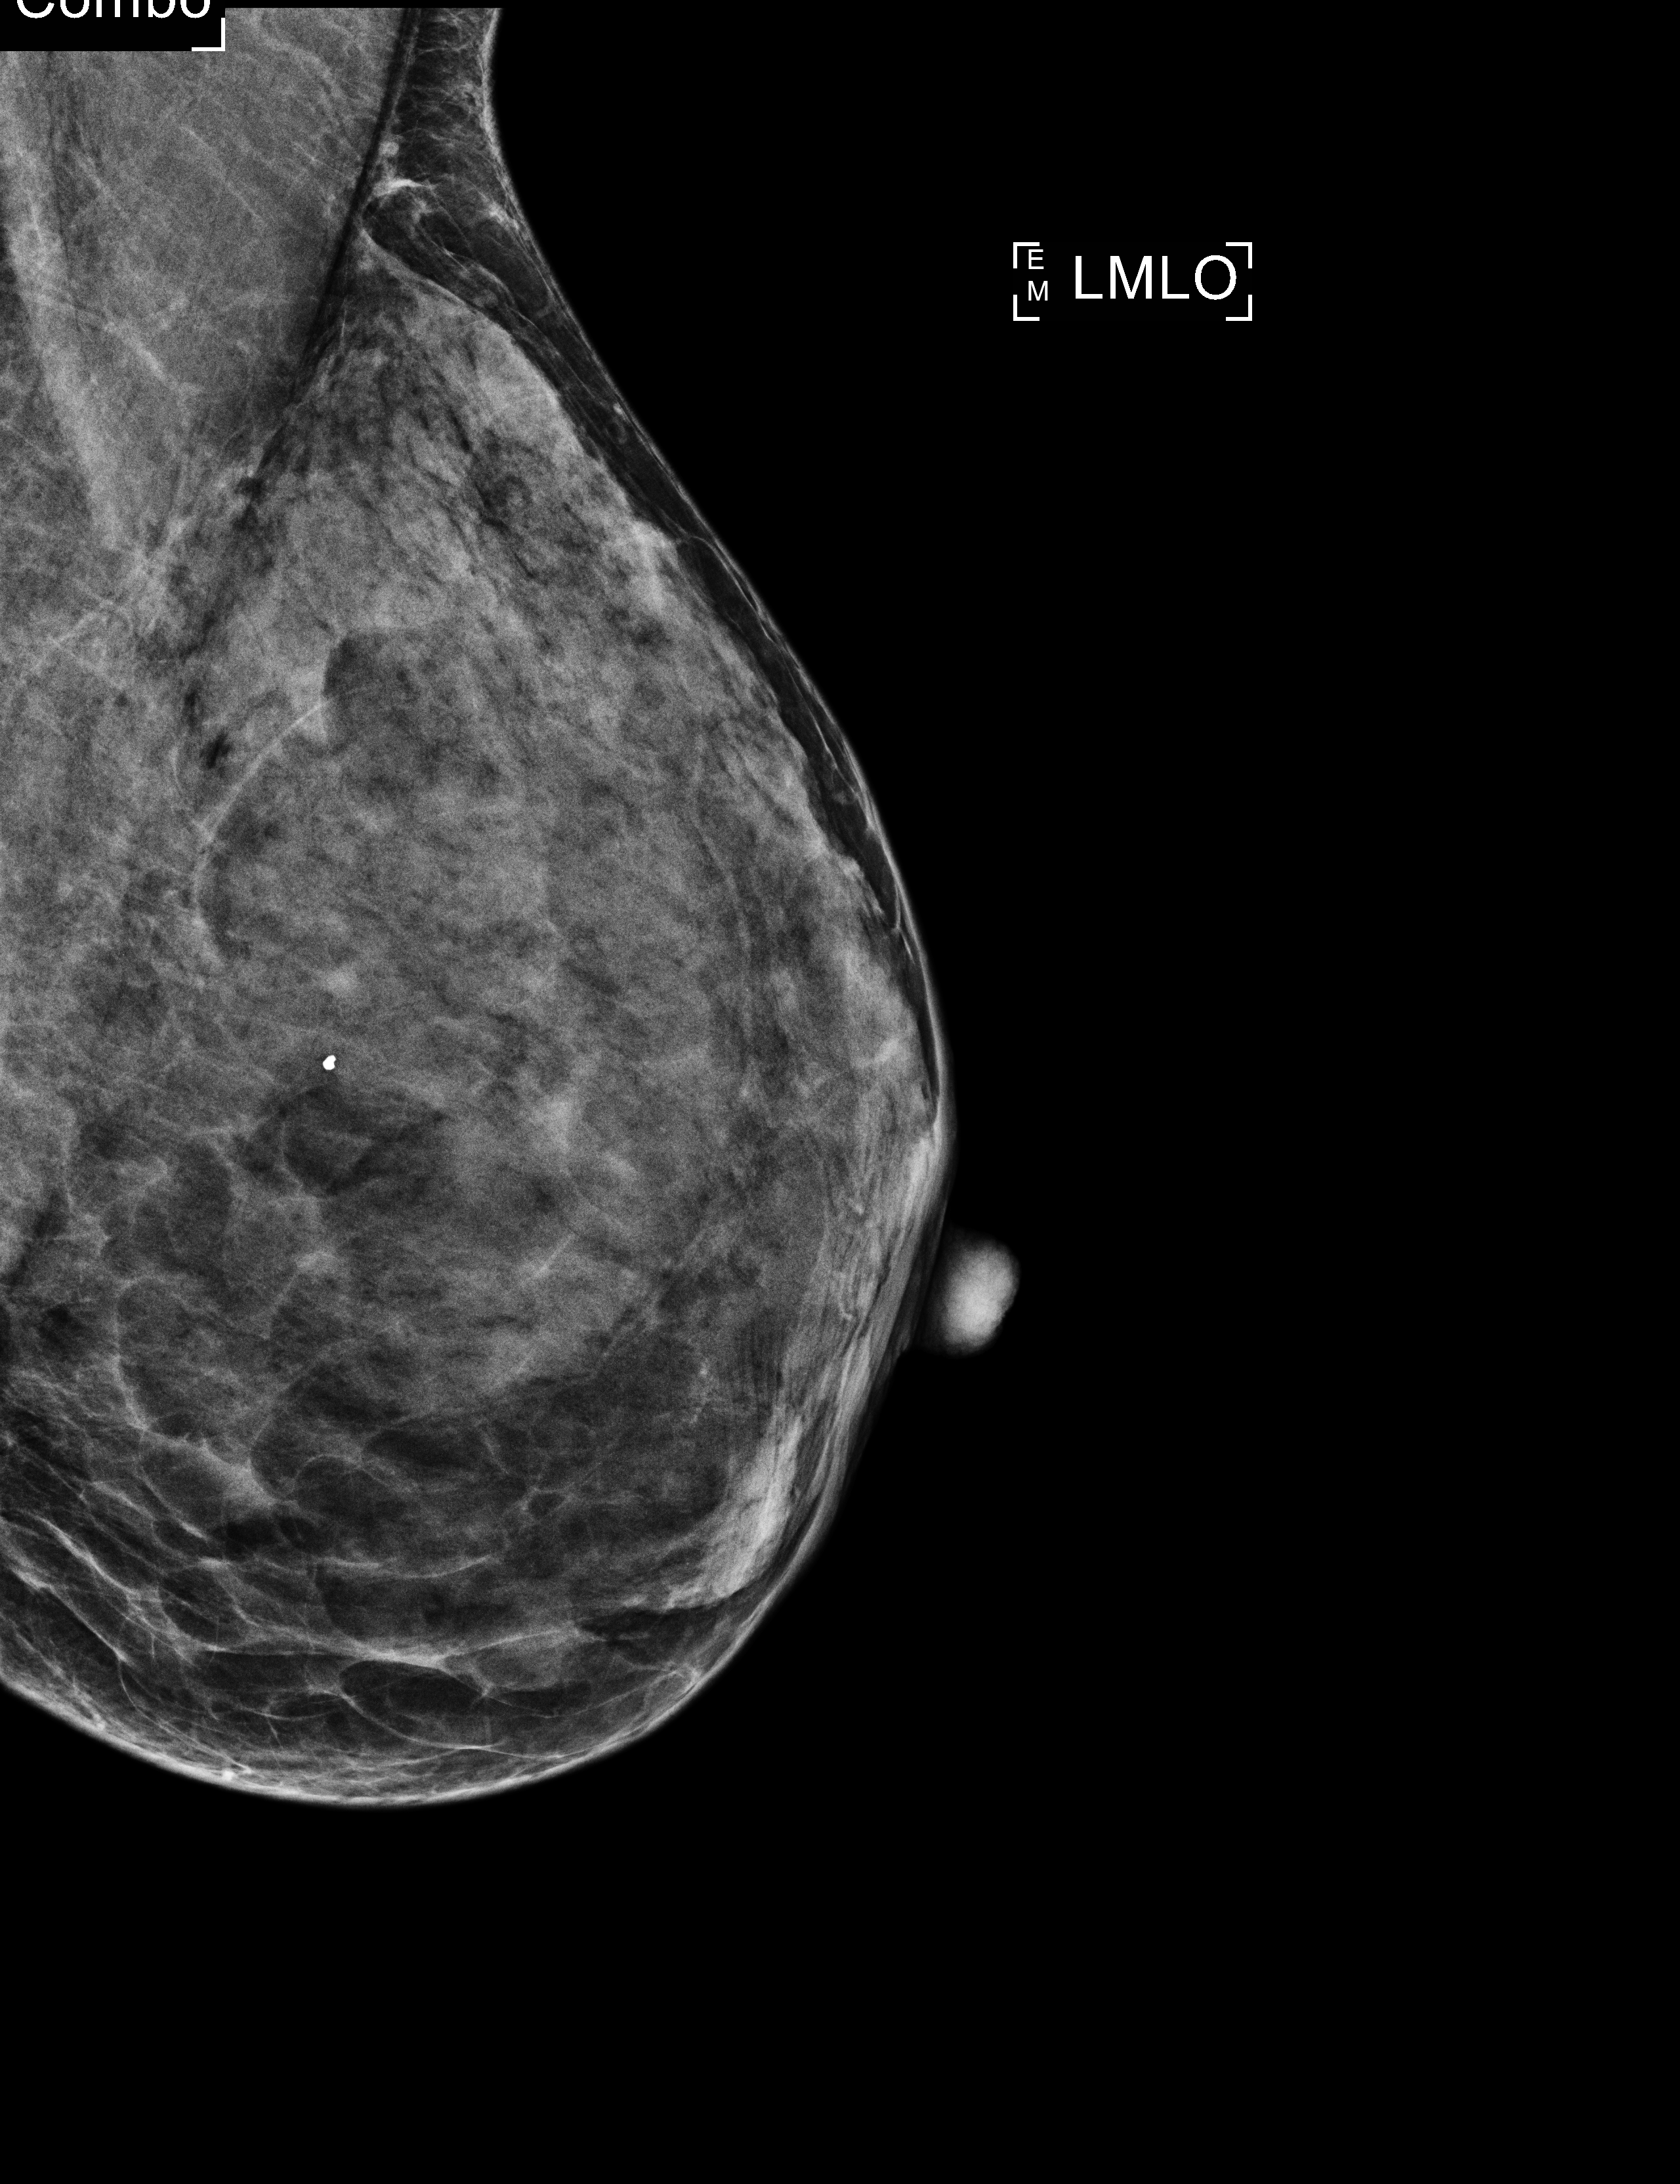
Full-field digital mammogram (FFDM), left breast, medio-lateral oblique projection, annual screening mammography examination. Patient aged 55 years (female).
BI-RADS breast density category at the screening exam (both breasts, scale 1–4): 4. Final BI-RADS category for the screening round (tomosynthesis exam, both breasts): category 2. Recall: no recall after this screen.